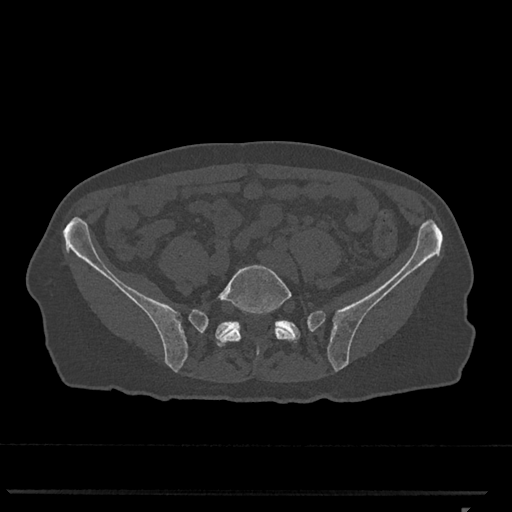
CT including the spine, one axial slice. Position 134 of 793 along the scan axis. 120 kVp. Bone window (W 1800 / L 400 HU). 0.5 mm slice thickness. 512 × 512 image matrix, field of view 380 × 380 mm. Female patient, age 62 years. Case-level facts recorded for this patient, not image findings: primary cancer: renal.
Structures marked on this image (semi-automatic segmentation, software-assisted and operator-edited):
- L5 vertebra: bounding box <216,265,297,360> (left, top, right, bottom; pixels)